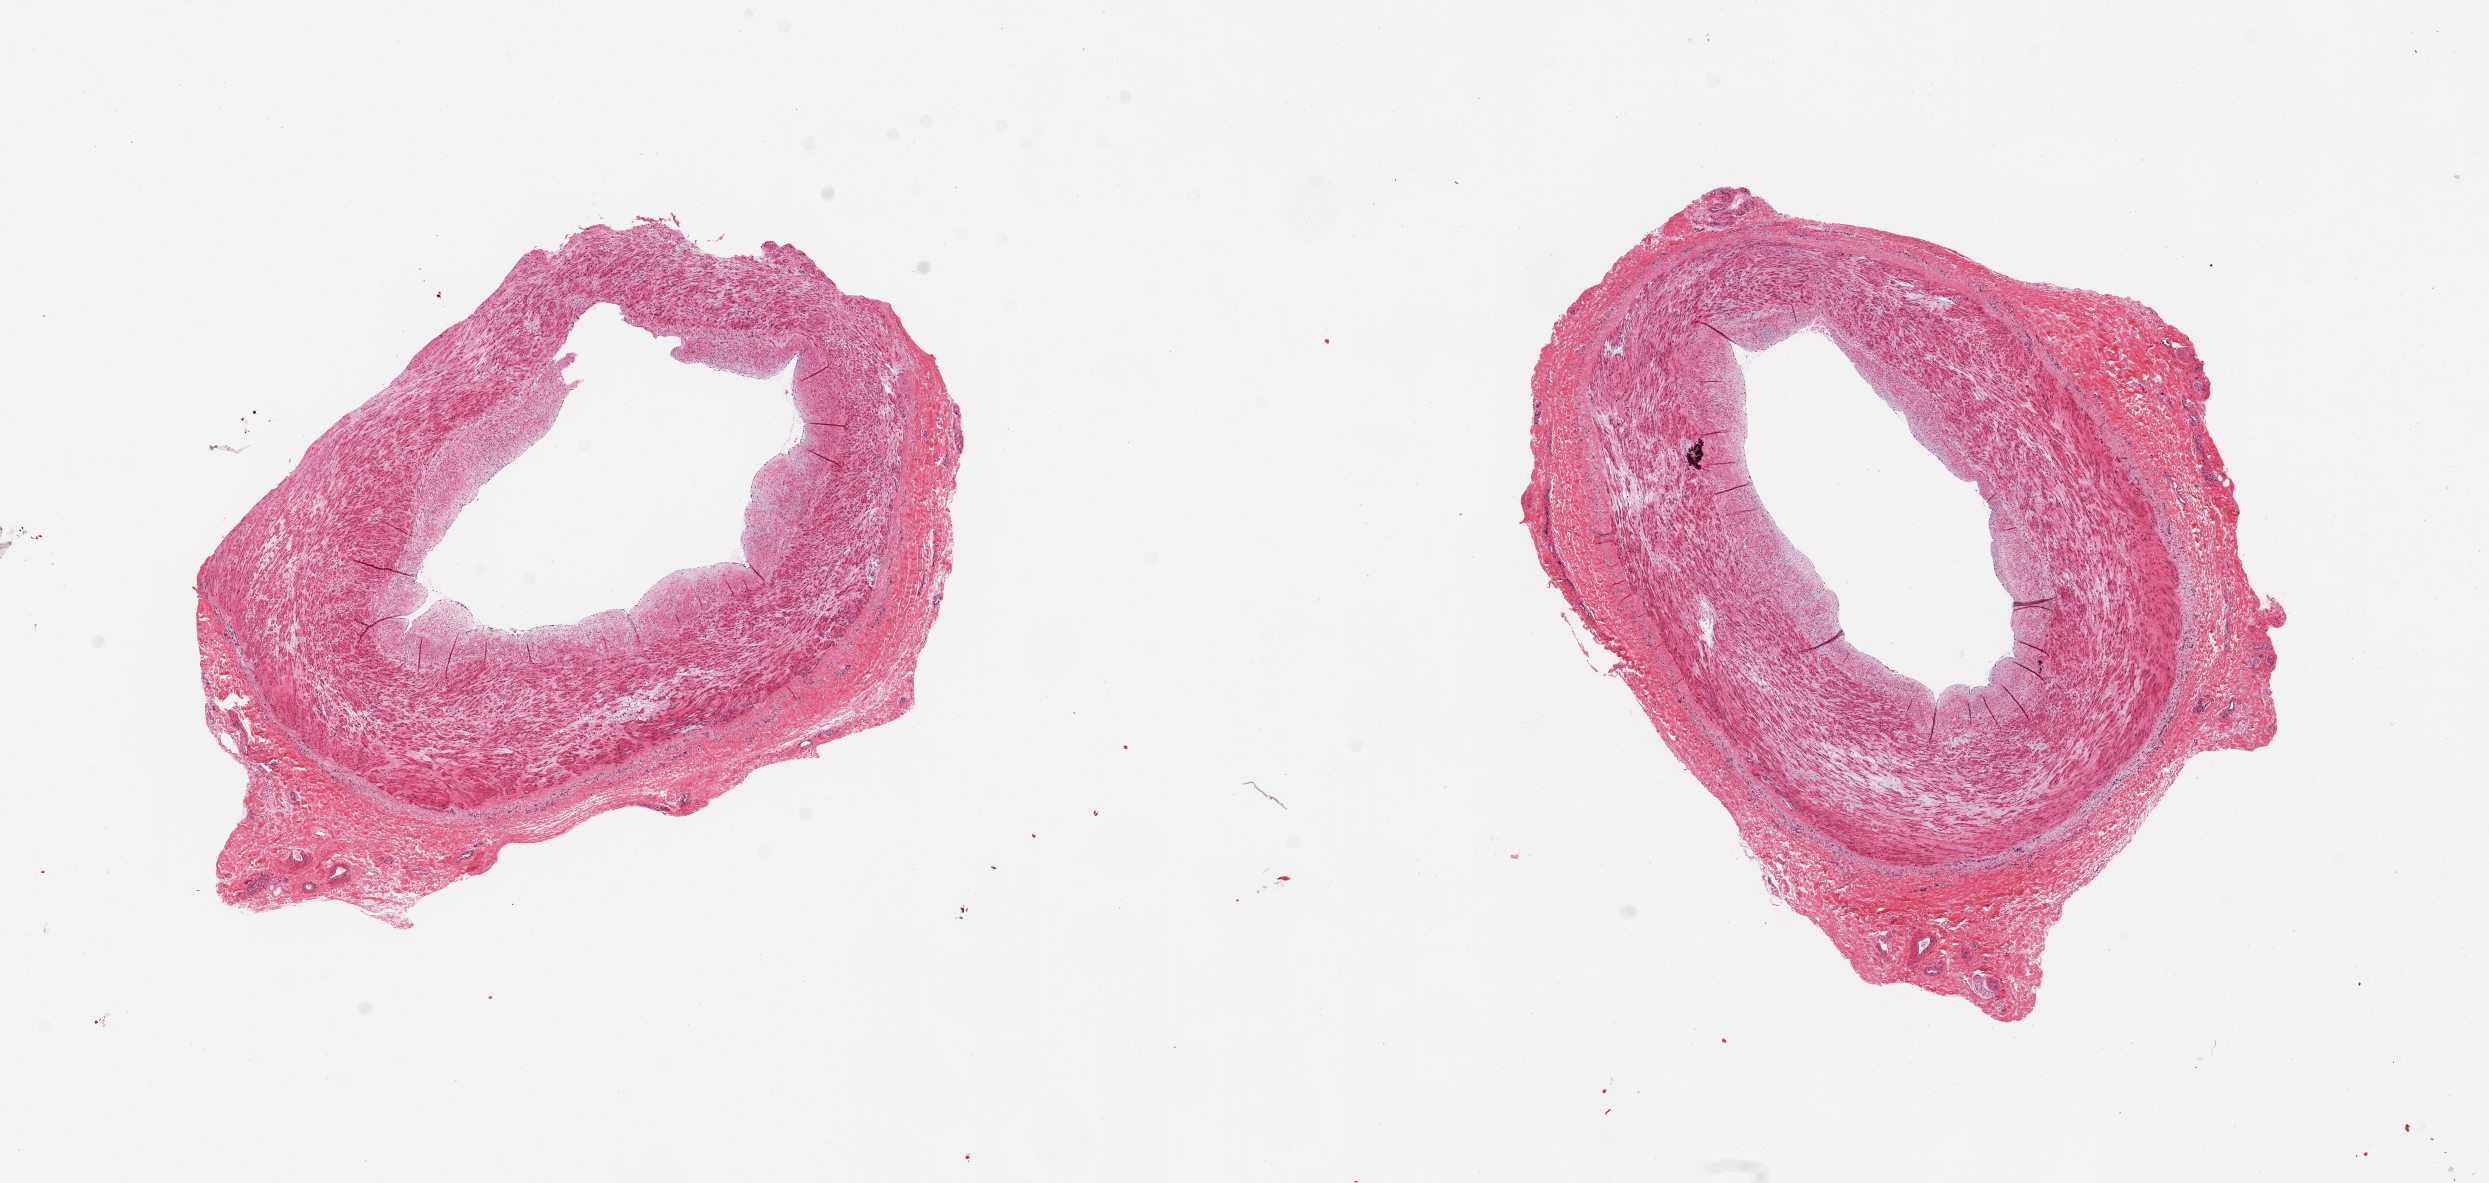
Whole-slide image, H&E stain, brightfield — shown as a low-resolution overview of the whole scanned area (about 19.7 x 9.4 mm, from a 20x scan). PAXgene-fixed paraffin-embedded (PFPE) section. Sampled site (target tissue): tibial artery. Tissue donor sample. Male donor.
- reviewer comment on this tissue sample: 2 pieces, rim of adherent fibrous tissue, up to ~1mm thick, generally good specimens